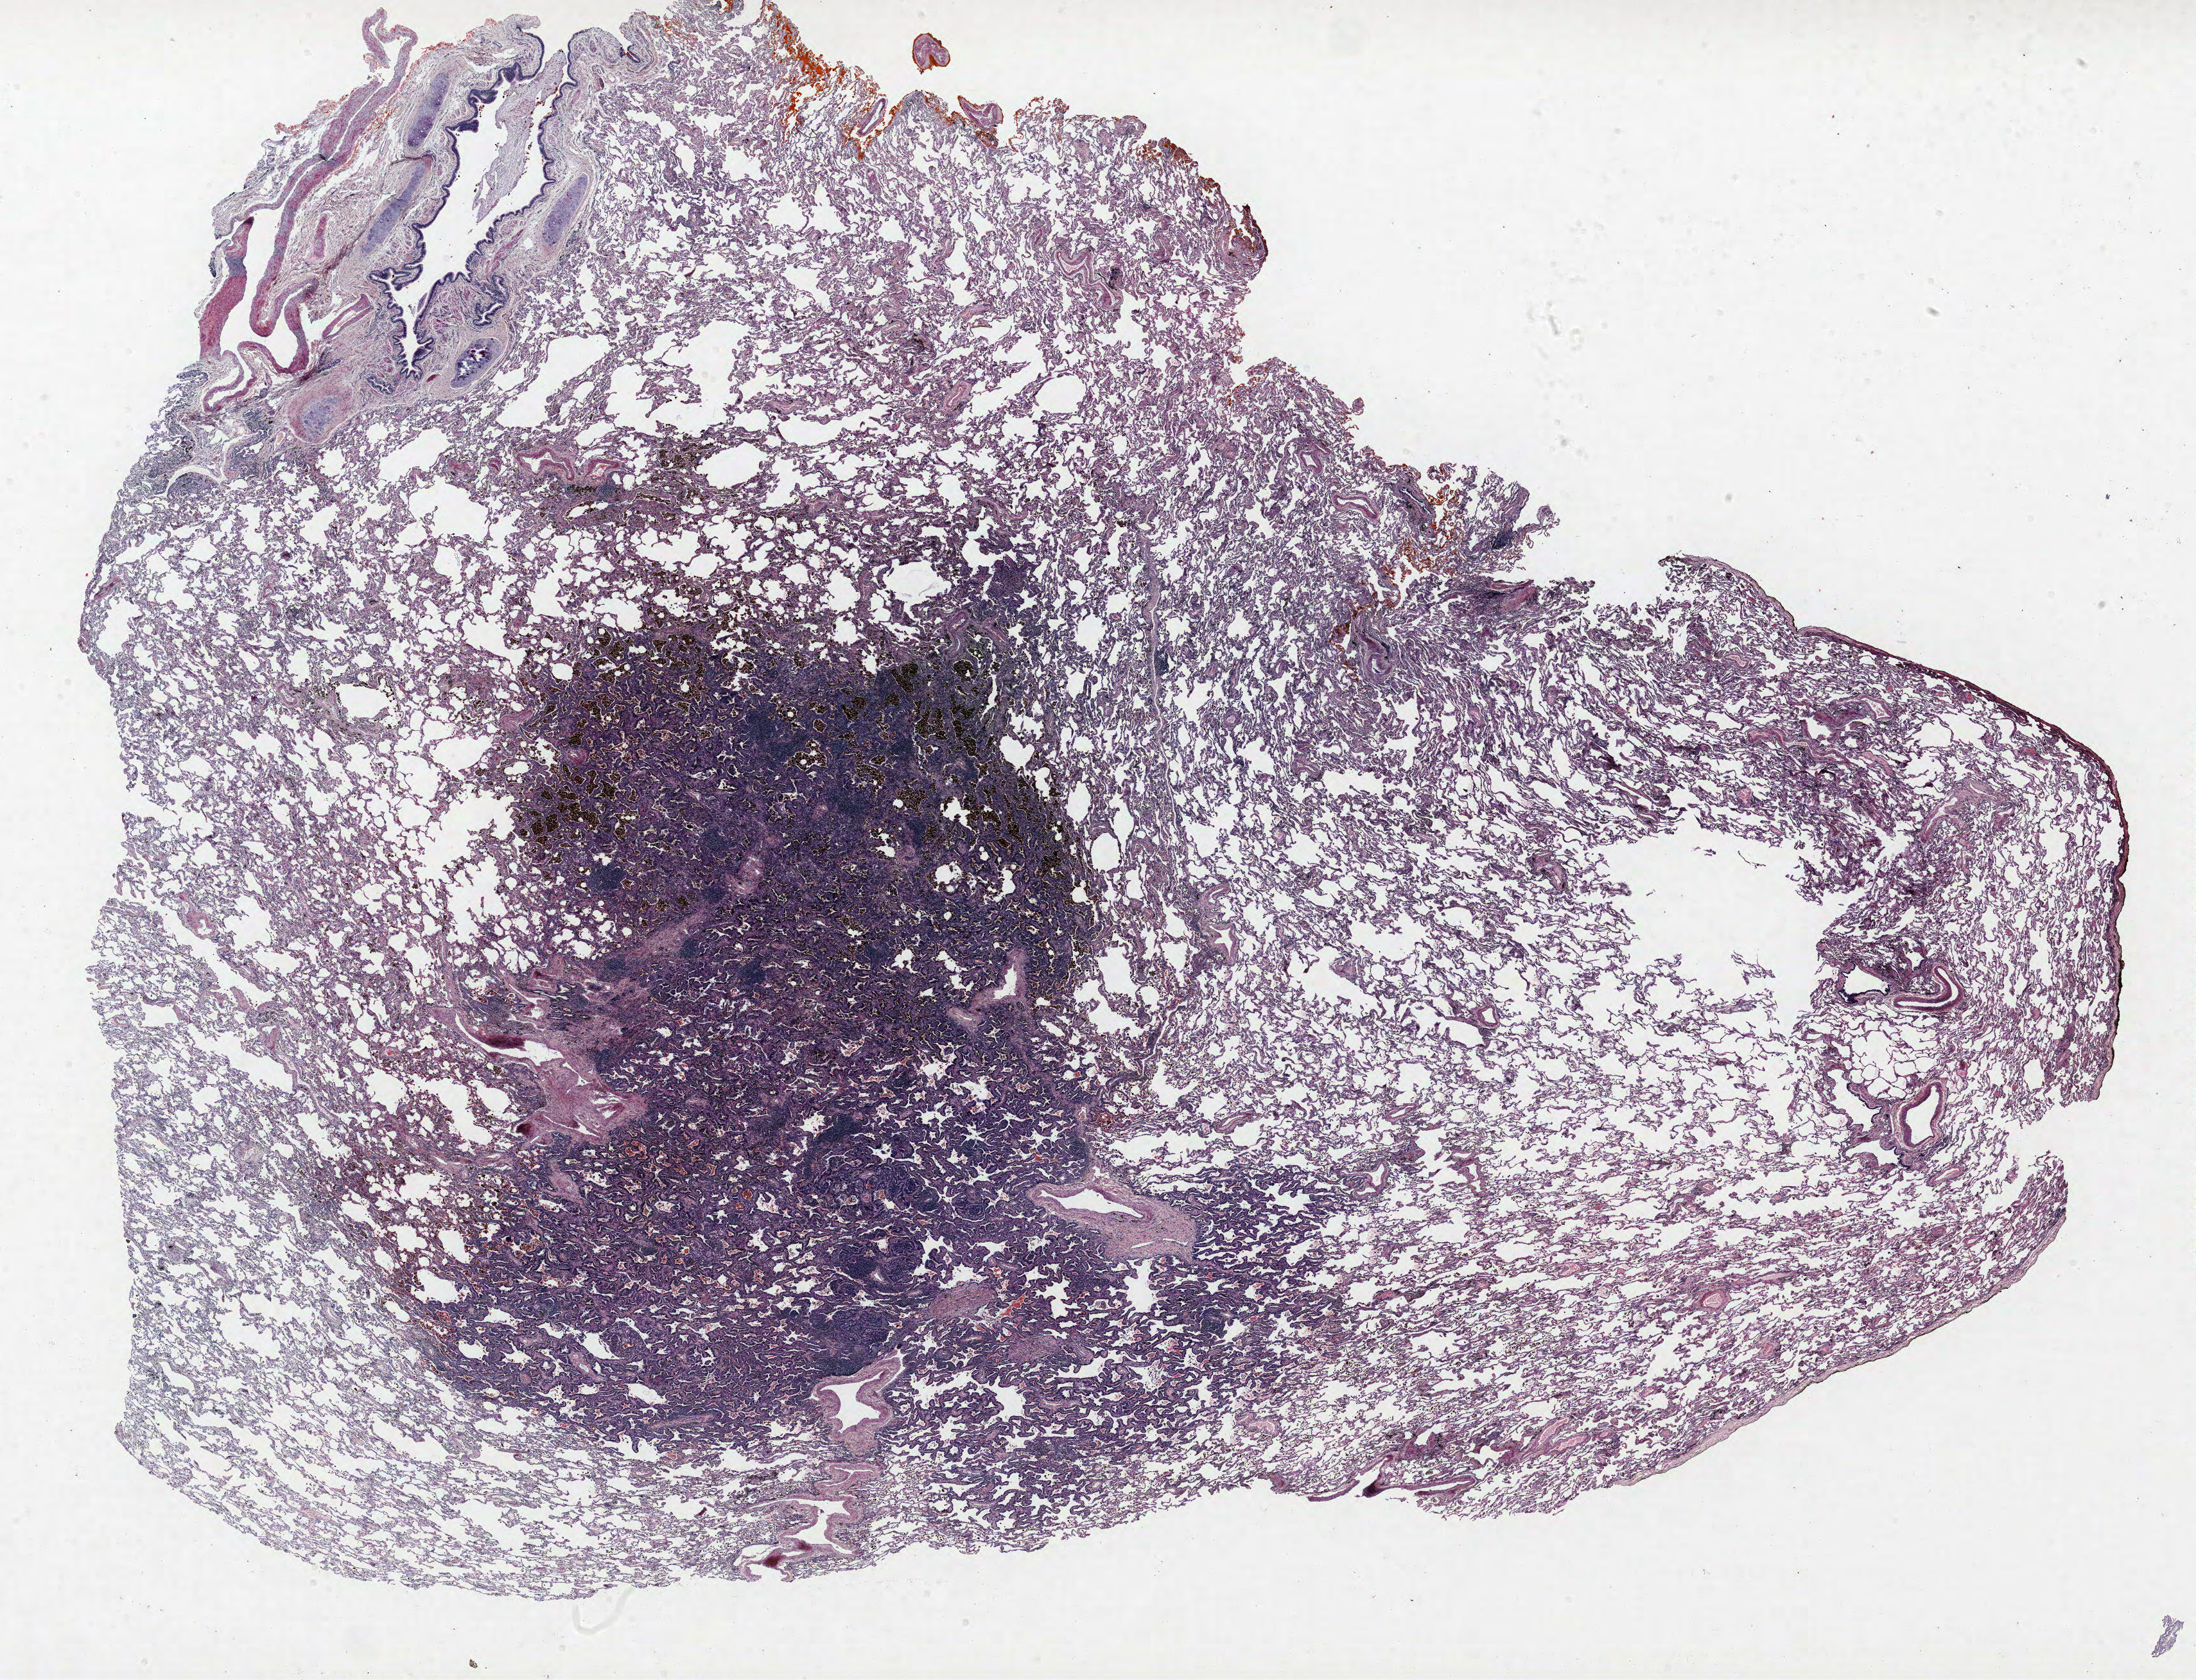
Whole-slide histology image, H&E, a low-resolution overview of the entire scanned area, about 27.4 x 20.9 mm (from a 40x scan). FFPE section. Lung tissue. Male, age 60 at enrolment. Former smoker at enrolment. Grade: well differentiated (G1).
Primary tumour location (clinical record): left upper lobe. ICD-O-3 topography: upper lobe of lung (C34.1). Tumour size (pathology): 16 mm. Participant's lung-cancer diagnosis: Bronchiolo-alveolar carcinoma, non-mucinous. Stage (AJCC 6th edition): IA.